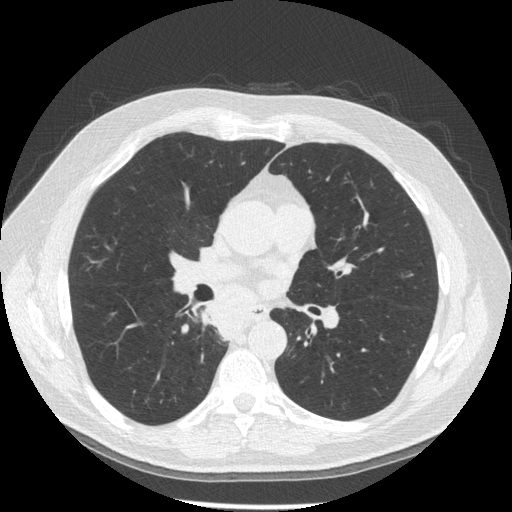
Low-dose screening chest CT, one axial slice; position 99 of 181 along the scan axis; 120 kVp; lung window (W 1500 / L -600 HU); 512 × 512 image matrix, field of view 370 × 370 mm.
Annotated regions visible in this slice (outlined manually by an expert reader):
- lesion 1 (tumor, lower lobe of right lung): box from (x=201, y=300) to (x=247, y=341) px